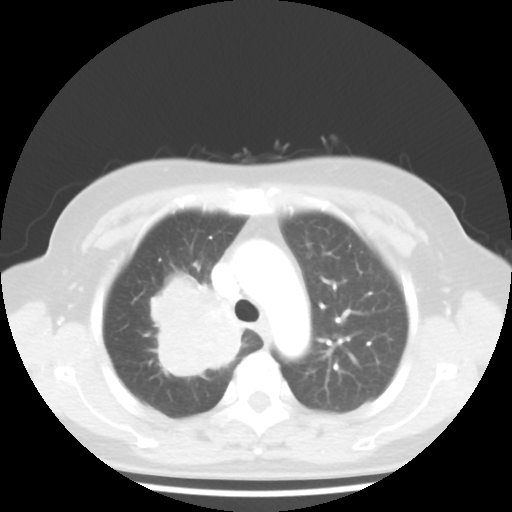
Chest CT, one axial slice. Slice 32 of 44 in the series (ordered by position). 100 kVp. Lung window (W 1500 / L -600 HU). 5 mm slice thickness. 512 × 512 image matrix, field of view 316 × 316 mm. Female patient, age 62 years. Case-level facts recorded for this patient, not image findings: clinical TNM (as recorded): T3 N0 M0; histopathological grade: G3.
Annotated regions visible in this slice (bounding box drawn by a radiologist):
- lung tumour (recorded histology: small cell carcinoma): box from (x=136, y=262) to (x=284, y=410) px